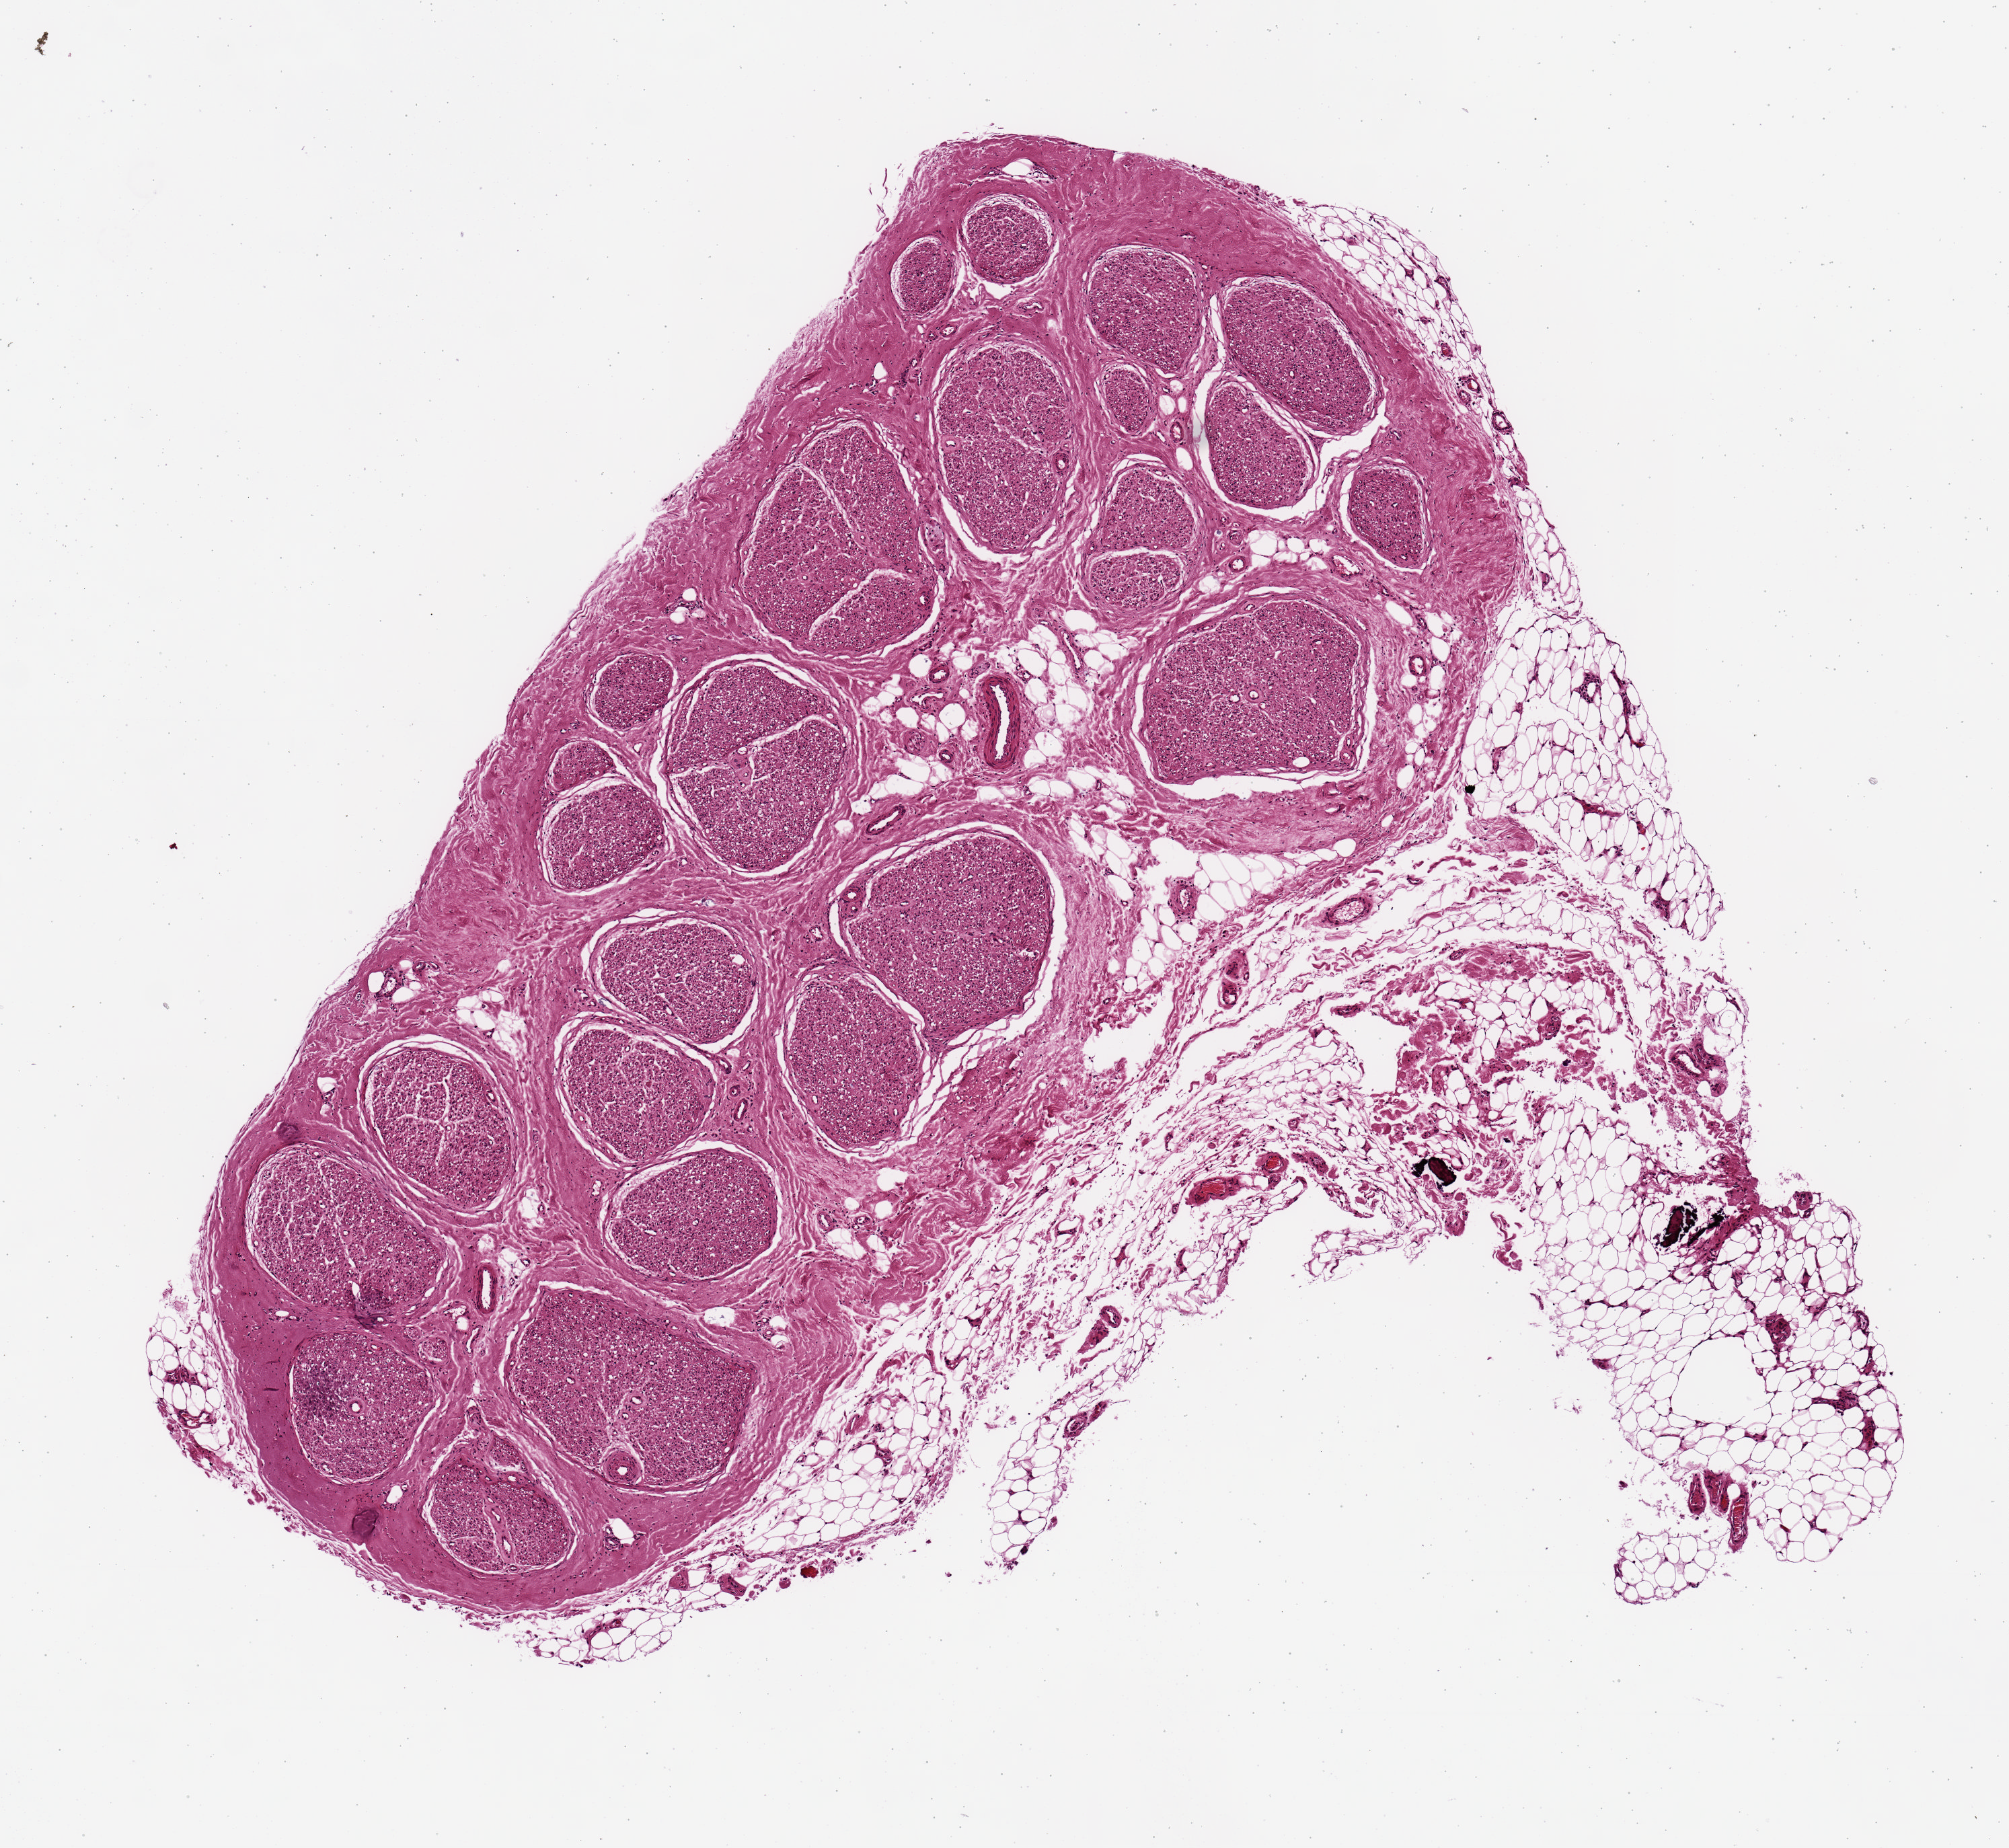
Whole-slide image, hematoxylin and eosin (H&E) stain, brightfield, low-resolution overview of the scanned area, about 5.9 x 5.4 mm (from a 20x scan); PAXgene-fixed, paraffin-embedded tissue; section of tibial nerve (target tissue); donor tissue sample. Donor: female.
Reviewer comment on this tissue sample: Nerve is approximately 80% of specimen; 20 is adipose (along one pole).